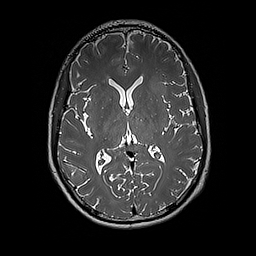
Brain MRI from a brain-tumour surgery series, one axial slice. Slice 96 of 192 in the series (ordered by position). 256 × 256 image matrix. Case-level facts recorded for this patient, not image findings: histopathology: Glioblastoma; WHO grade: 4; IDH mutation: no.
Outlined on this slice (outlined manually by an expert reader):
- tumour: bounding box <140,76,171,96> (left, top, right, bottom; pixels)